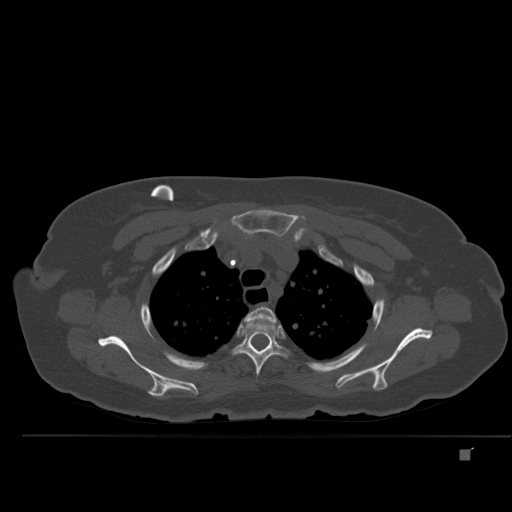
CT including the spine, one axial slice. Slice 381 of 477 in the series (ordered by position). Bone window (W 1800 / L 400 HU). 1.5 mm slice thickness. 512 × 512 image matrix. Female patient, age 74 years. From the clinical record (not read from this slice): primary cancer: colon.
Structures marked on this image (semi-automatic segmentation, software-assisted and operator-edited):
- T2 vertebra: bounding box (x1, y1, x2, y2) in pixels: (244, 307, 277, 322)
- T3 vertebra: (232, 318, 288, 376)